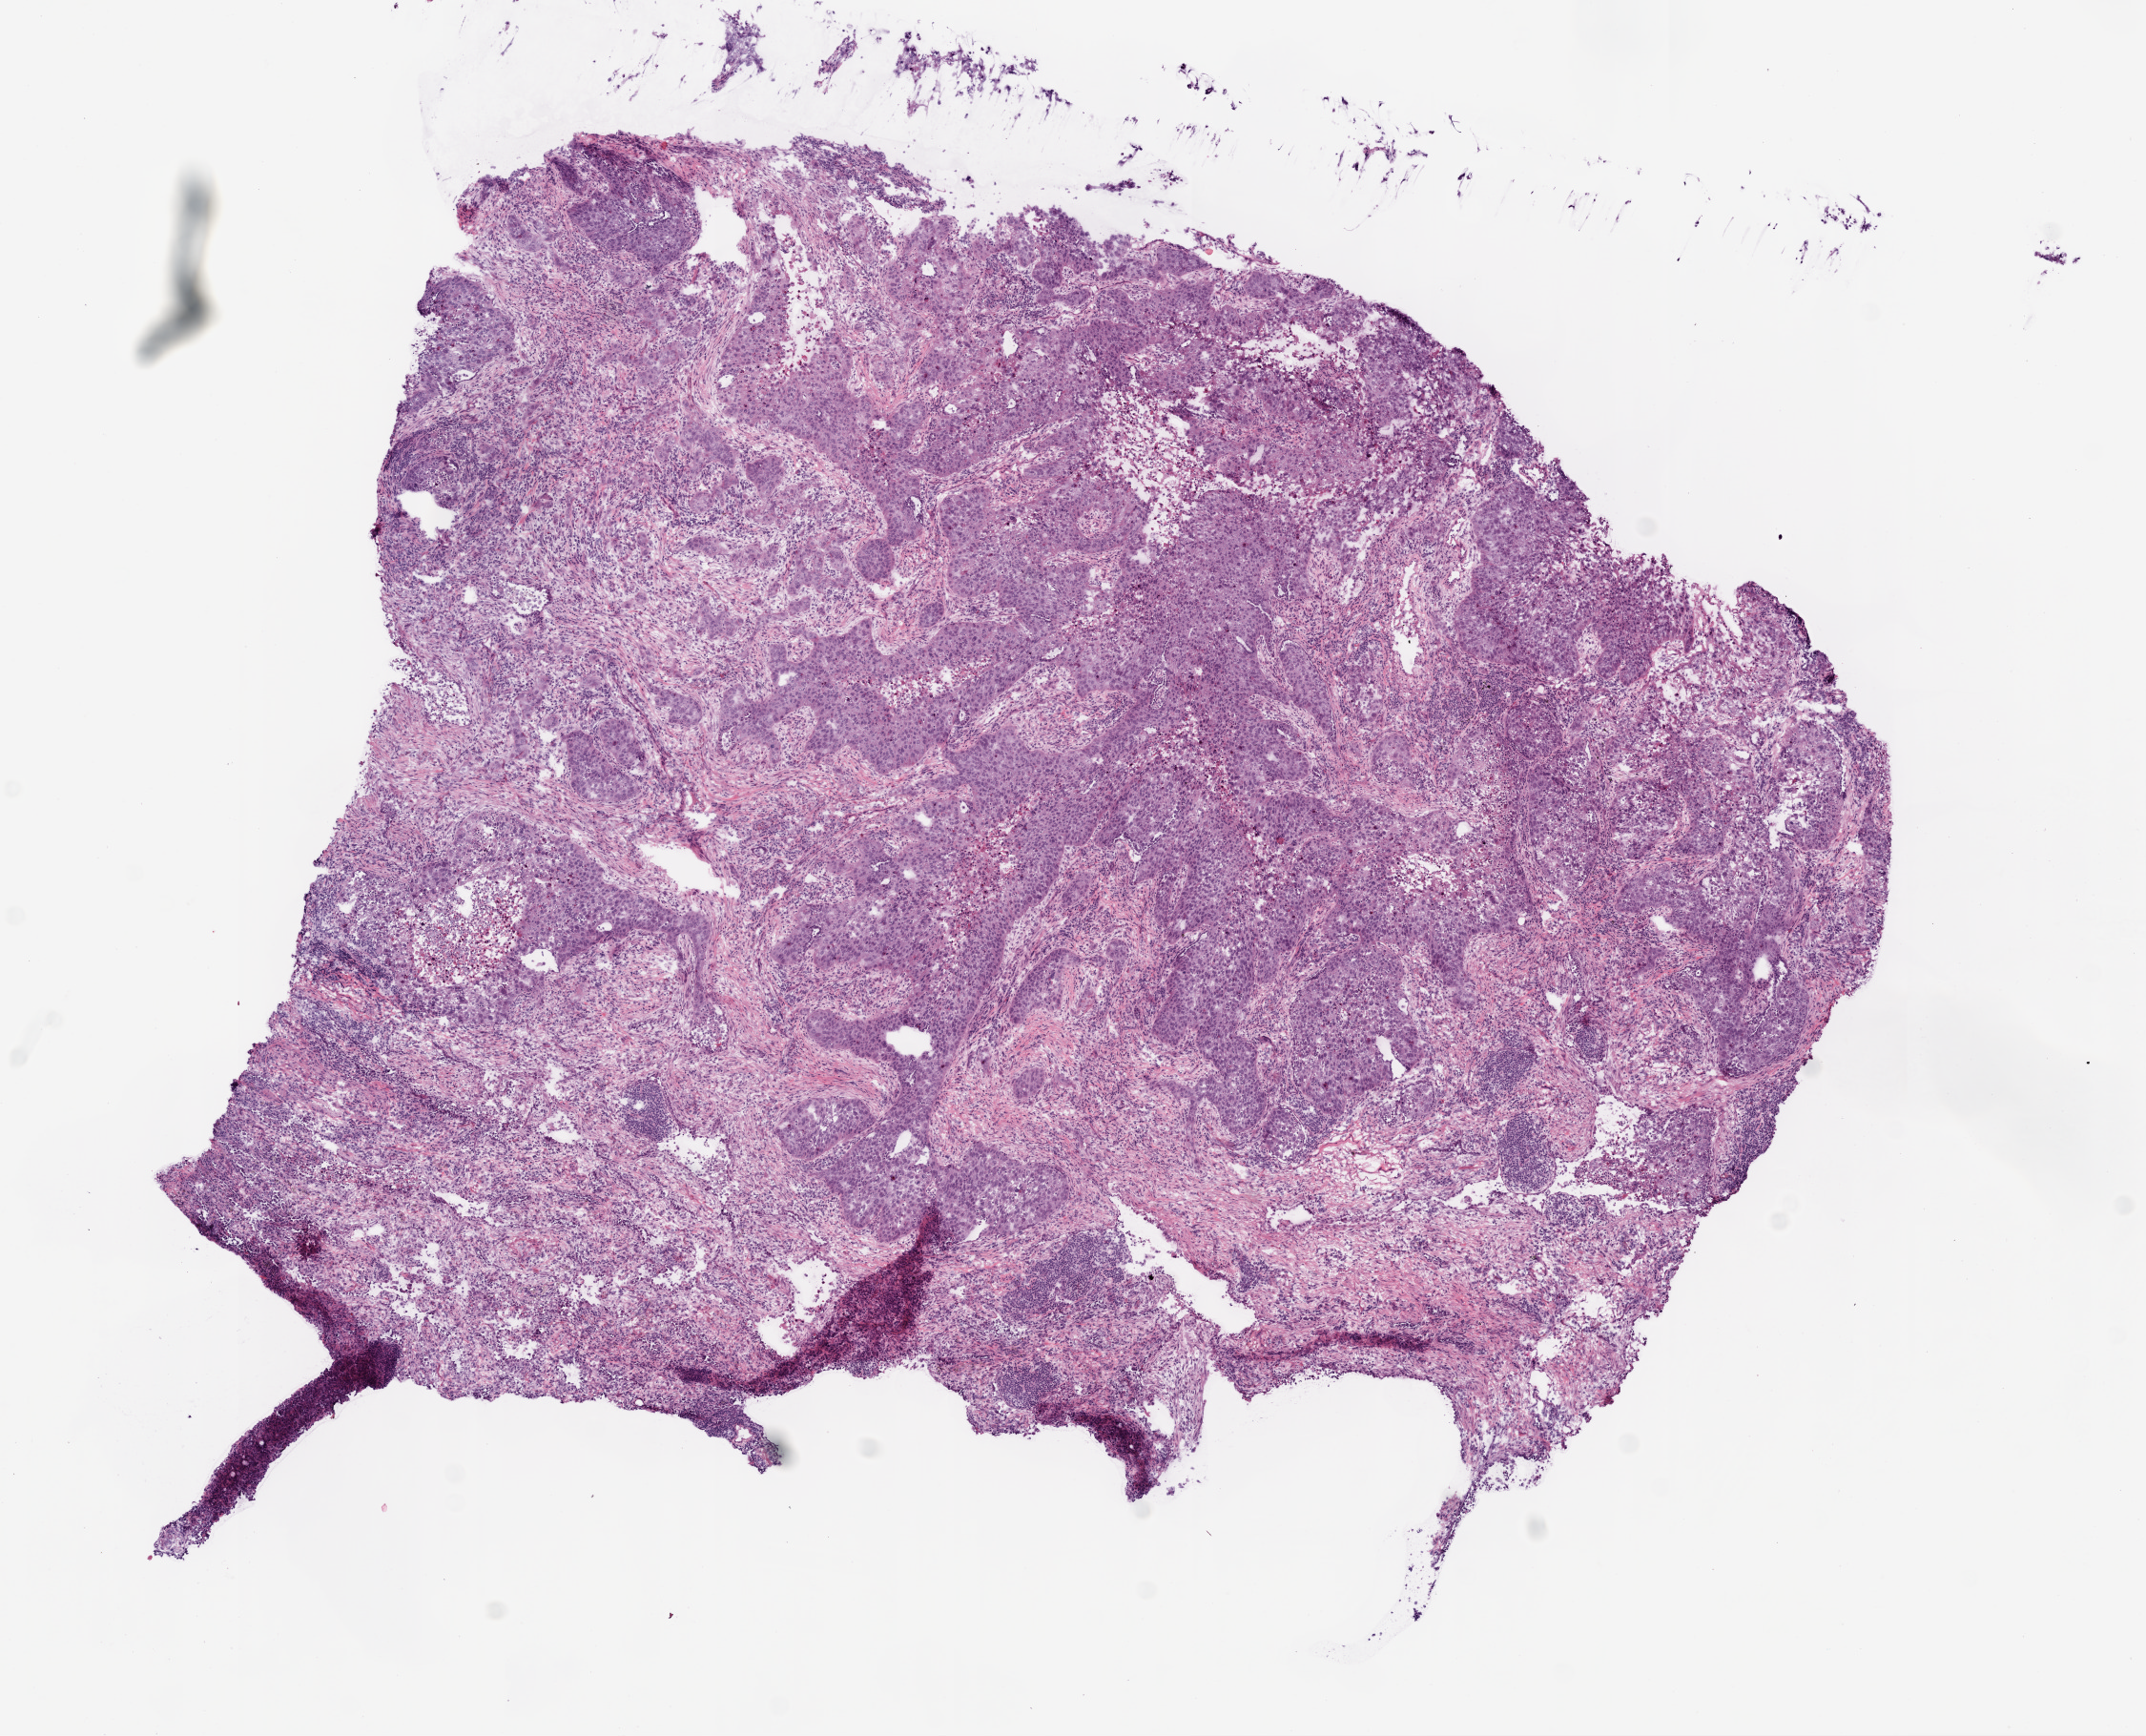
Hematoxylin and eosin (H&E) stained whole-slide image, whole scanned area (about 9.0 x 7.3 mm, acquisition: 20x scan) shown as a low-resolution overview. Frozen section from the top of the tissue portion. Primary tumour sample from the lung. Male, age 69 years at initial diagnosis. Composition of this section per pathologist review: tumour cells 82%, tumour nuclei 60%, normal cells 0%, stromal cells 10%, necrosis 8%.
Diagnosis: Squamous cell carcinoma, NOS (lower lobe, lung). AJCC pathologic stage: IB (5th edition). Laterality: left.